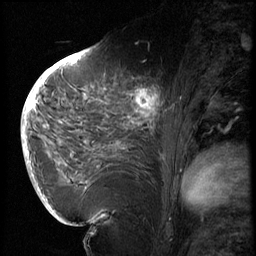
Breast MRI (dynamic contrast-enhanced), one sagittal slice; slice 33 of 72 in the series (ordered by position); 3 images stored at this slice position (order not interpretable as contrast timing); 1.5 T; TE 4.2 ms, TR 8.9 ms; 256 × 256 image matrix, field of view 200 × 200 mm. Patient: female, 56 years. Case-level facts recorded for this patient, not image findings: setting: breast cancer imaged before/during neoadjuvant chemotherapy.
Annotated regions visible in this slice (semi-automatic segmentation, software-assisted and operator-edited):
- analysis volume of interest (the breast-tissue region the enhancement analysis was run in; not a lesion): box from (x=114, y=76) to (x=177, y=138) px
- tumour enhancement mask (voxels above the 140 % enhancement threshold inside the analysis volume of interest): (x=134, y=88)–(x=163, y=125)